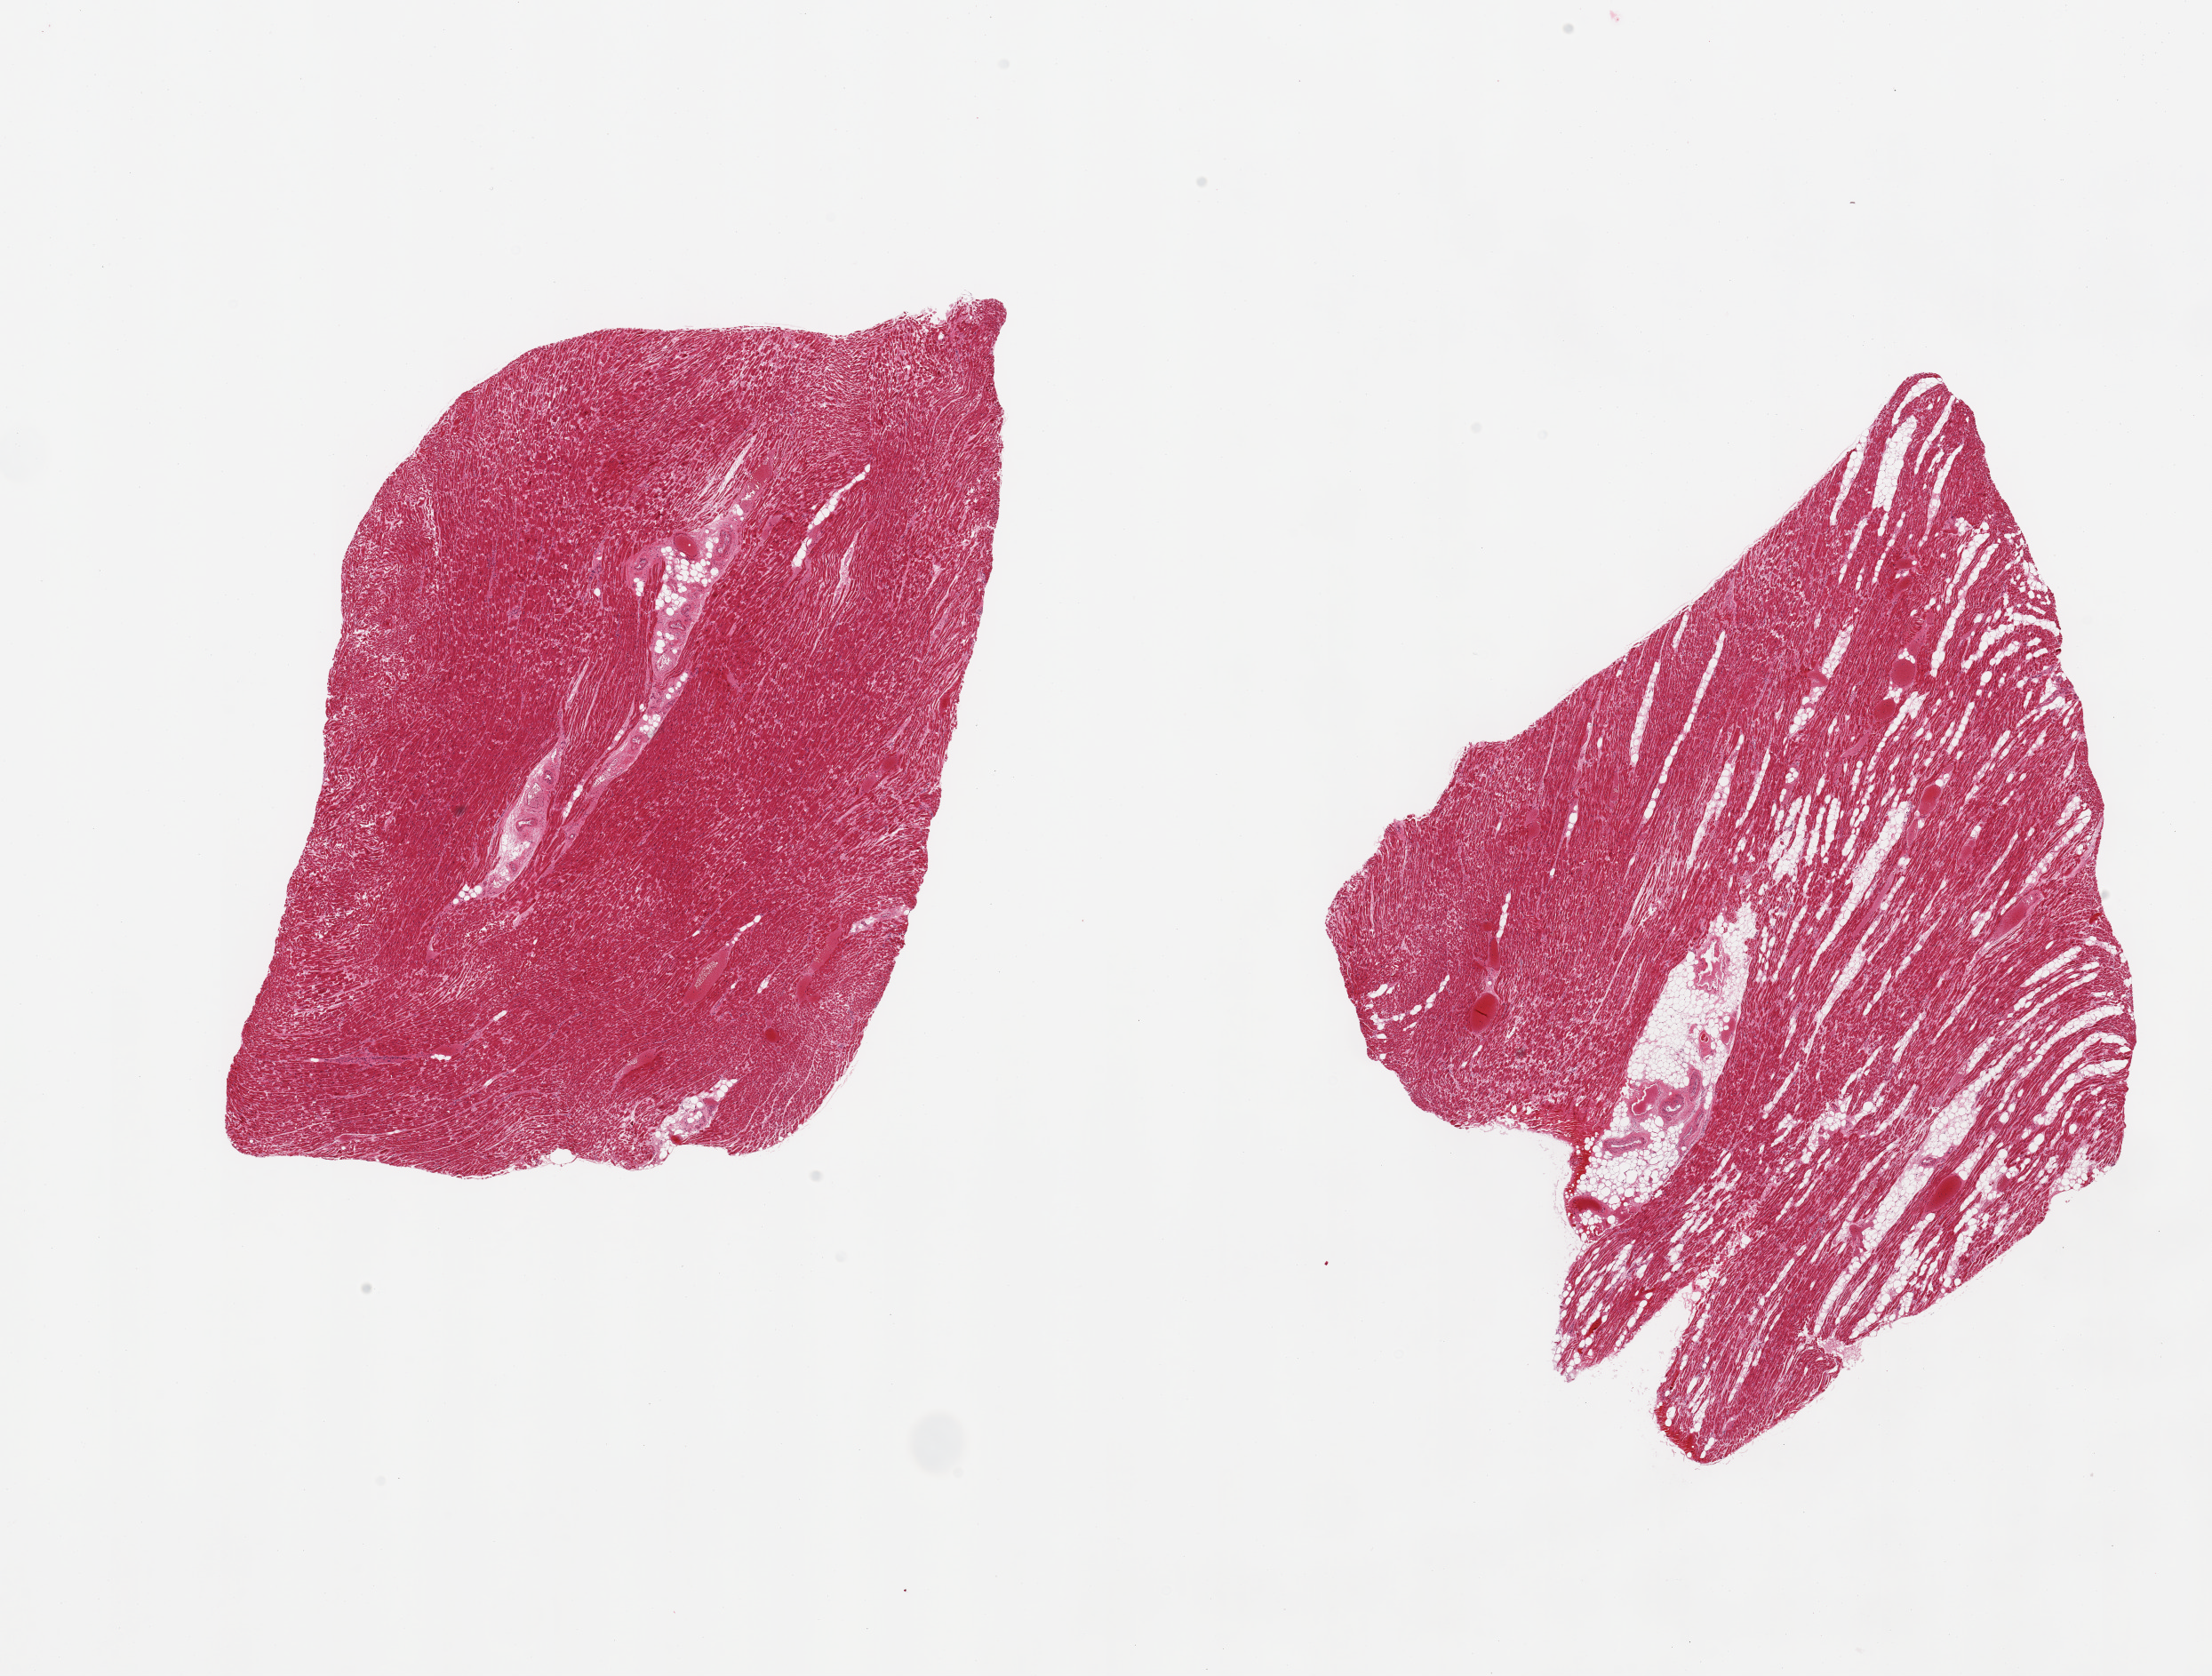
Haematoxylin and eosin whole-slide image — a low-resolution overview of the entire scanned area, about 19.7 x 14.9 mm; PAXgene-fixed paraffin-embedded (PFPE) section; target tissue: heart; tissue donor sample. Female donor.
Pathologist's review note for this sample: 2 pieces; one piece is 10-20% internal fat.